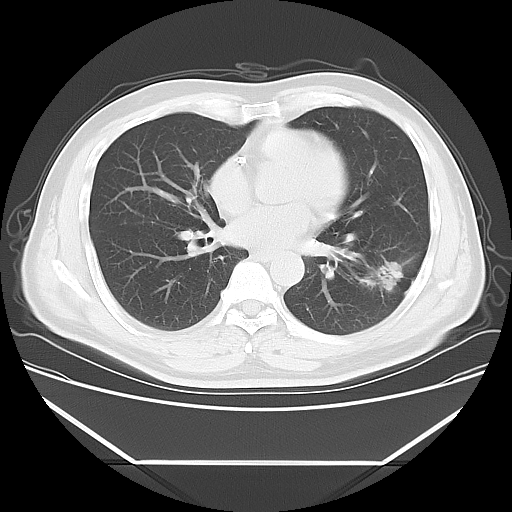
Chest CT, one axial slice. Position 27 of 57 along the scan axis. 120 kVp. Lung window (W 1500 / L -600 HU). 5 mm slice thickness. 512 × 512 image matrix, field of view 384 × 384 mm. Patient: male, 53 years. Case-level facts recorded for this patient, not image findings: clinical TNM (as recorded): T1c N0 M0; histopathological grade: G2-3.
Annotated regions visible in this slice (bounding box drawn by a radiologist):
- lung tumour (recorded histology: adenocarcinoma): bounding box [x1, y1, x2, y2] px = [355, 256, 402, 300]